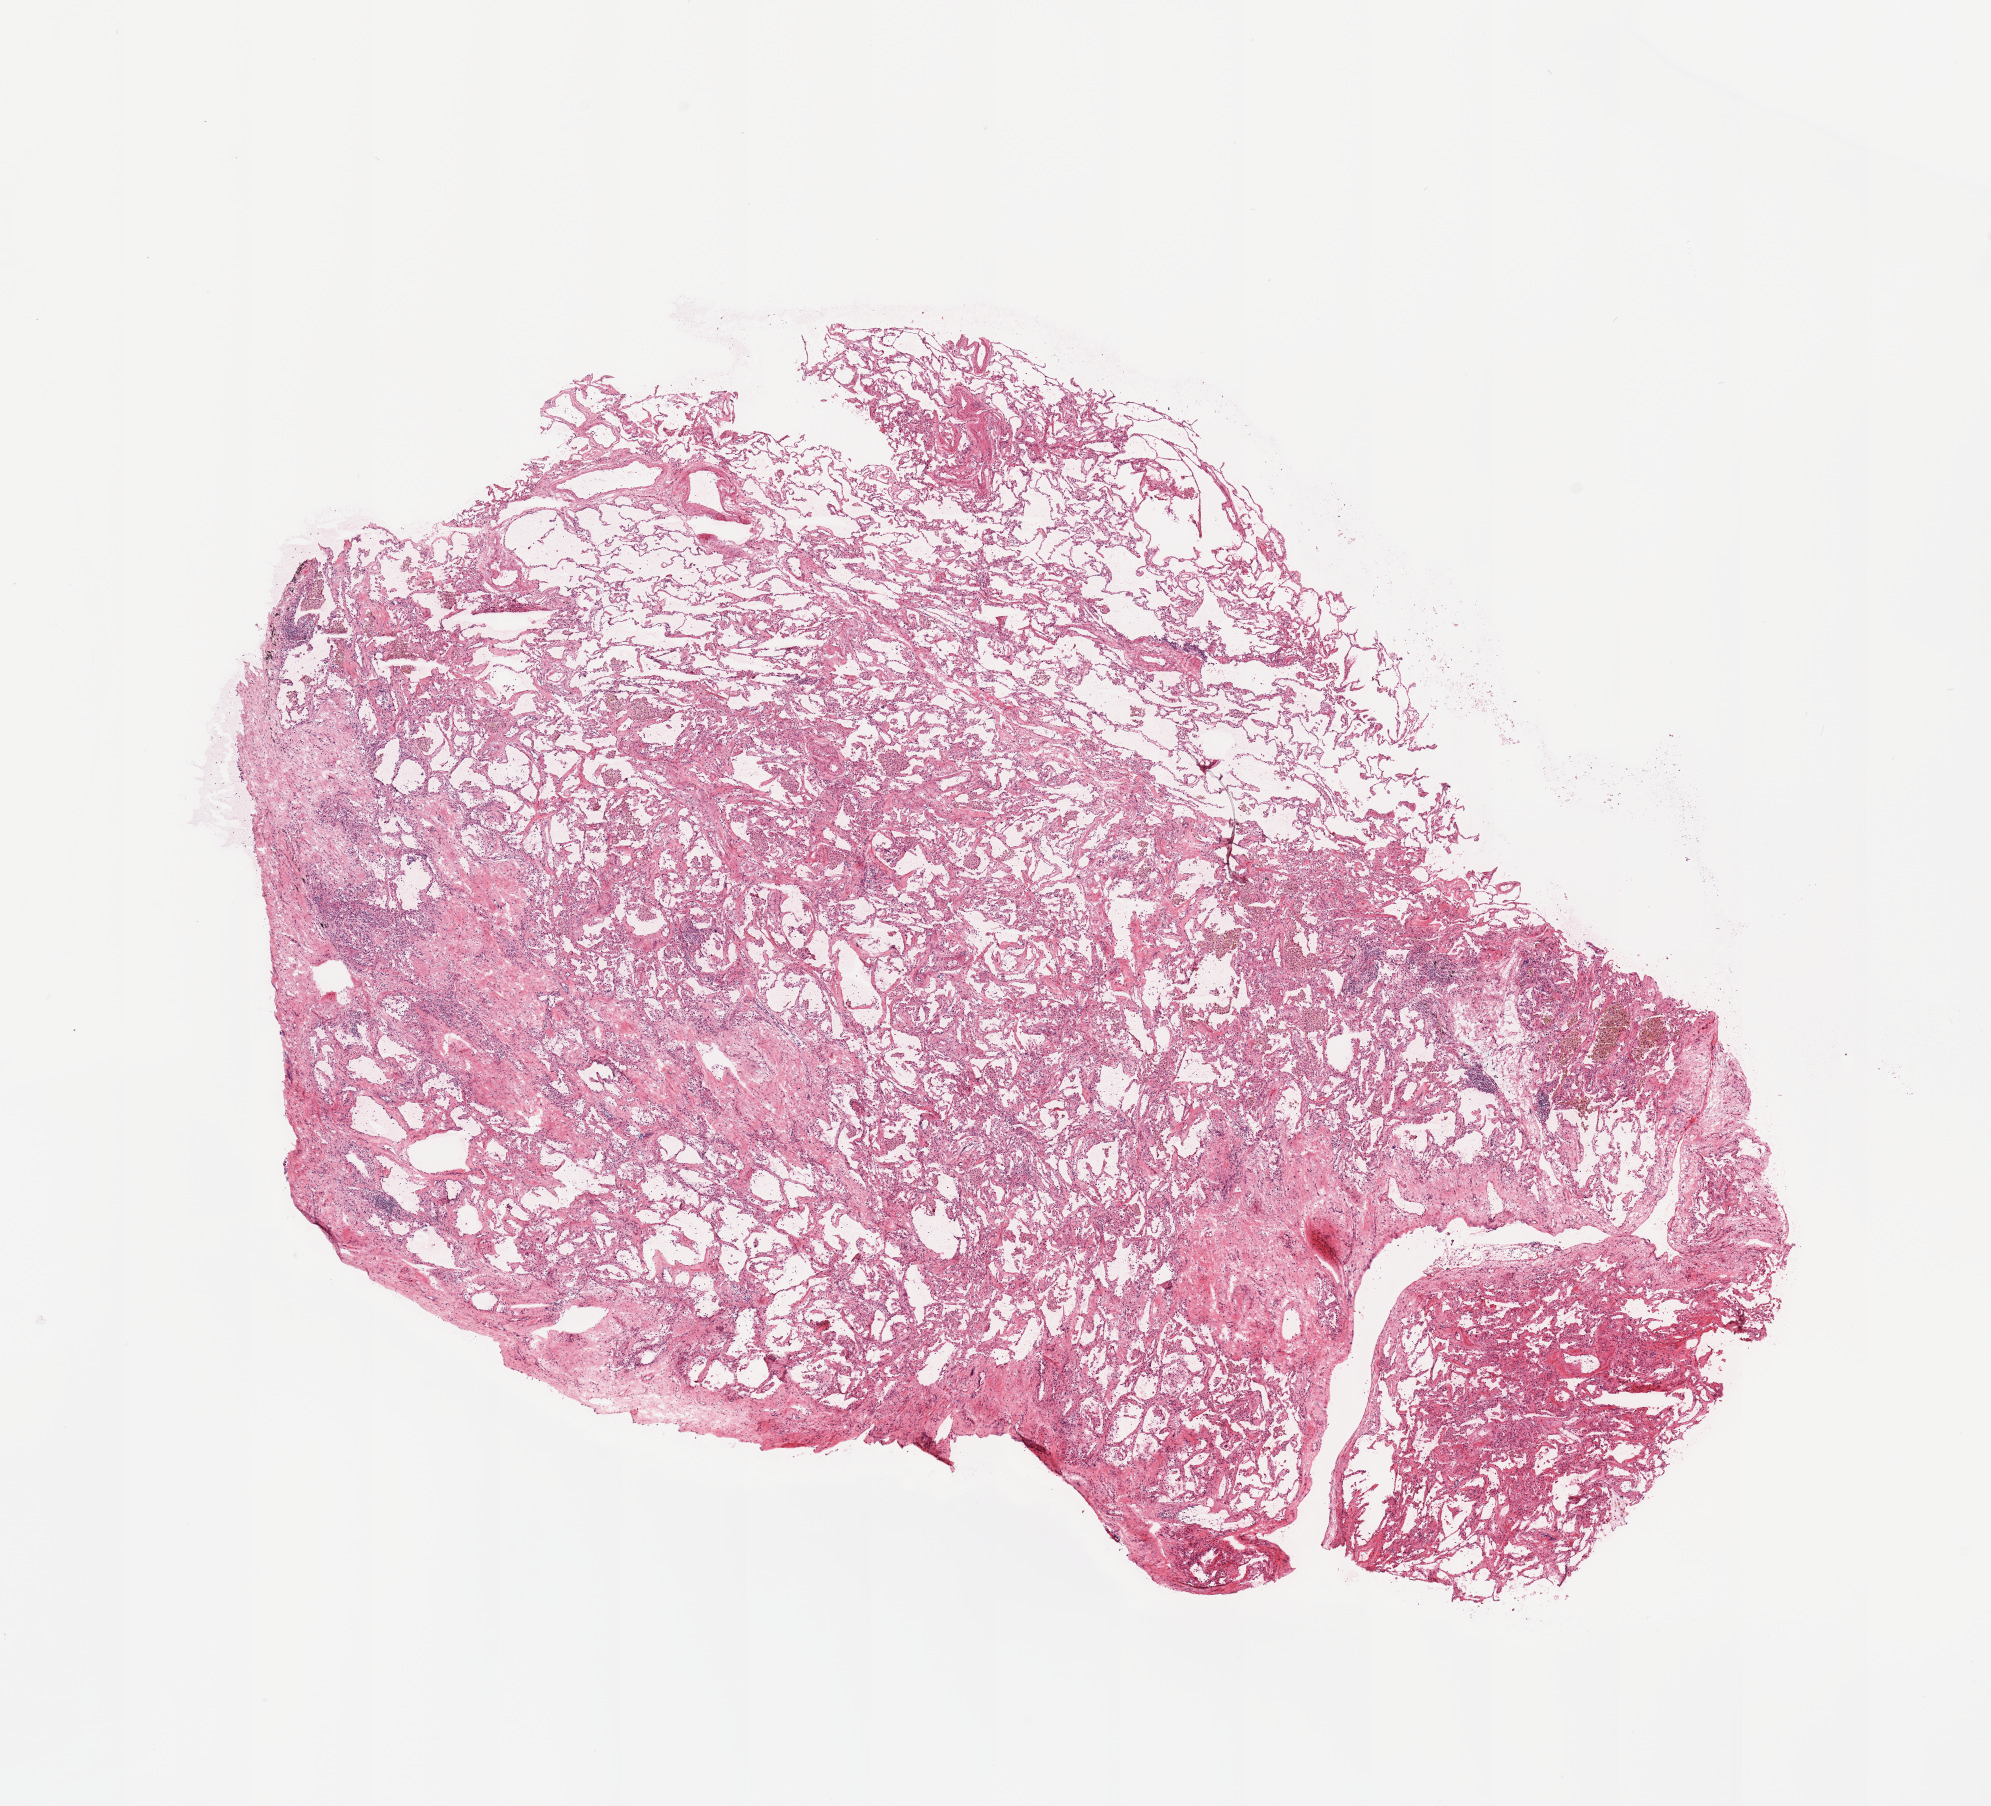
Digitized H&E-stained tissue section (whole slide) — low-resolution overview of the scanned area, about 15.8 x 14.3 mm. Lung, normal (non-tumour) tissue. Female, 72 y/o.
This section: normal (non-tumour) tissue from the same patient. Patient diagnosis: Adenocarcinoma, NOS.